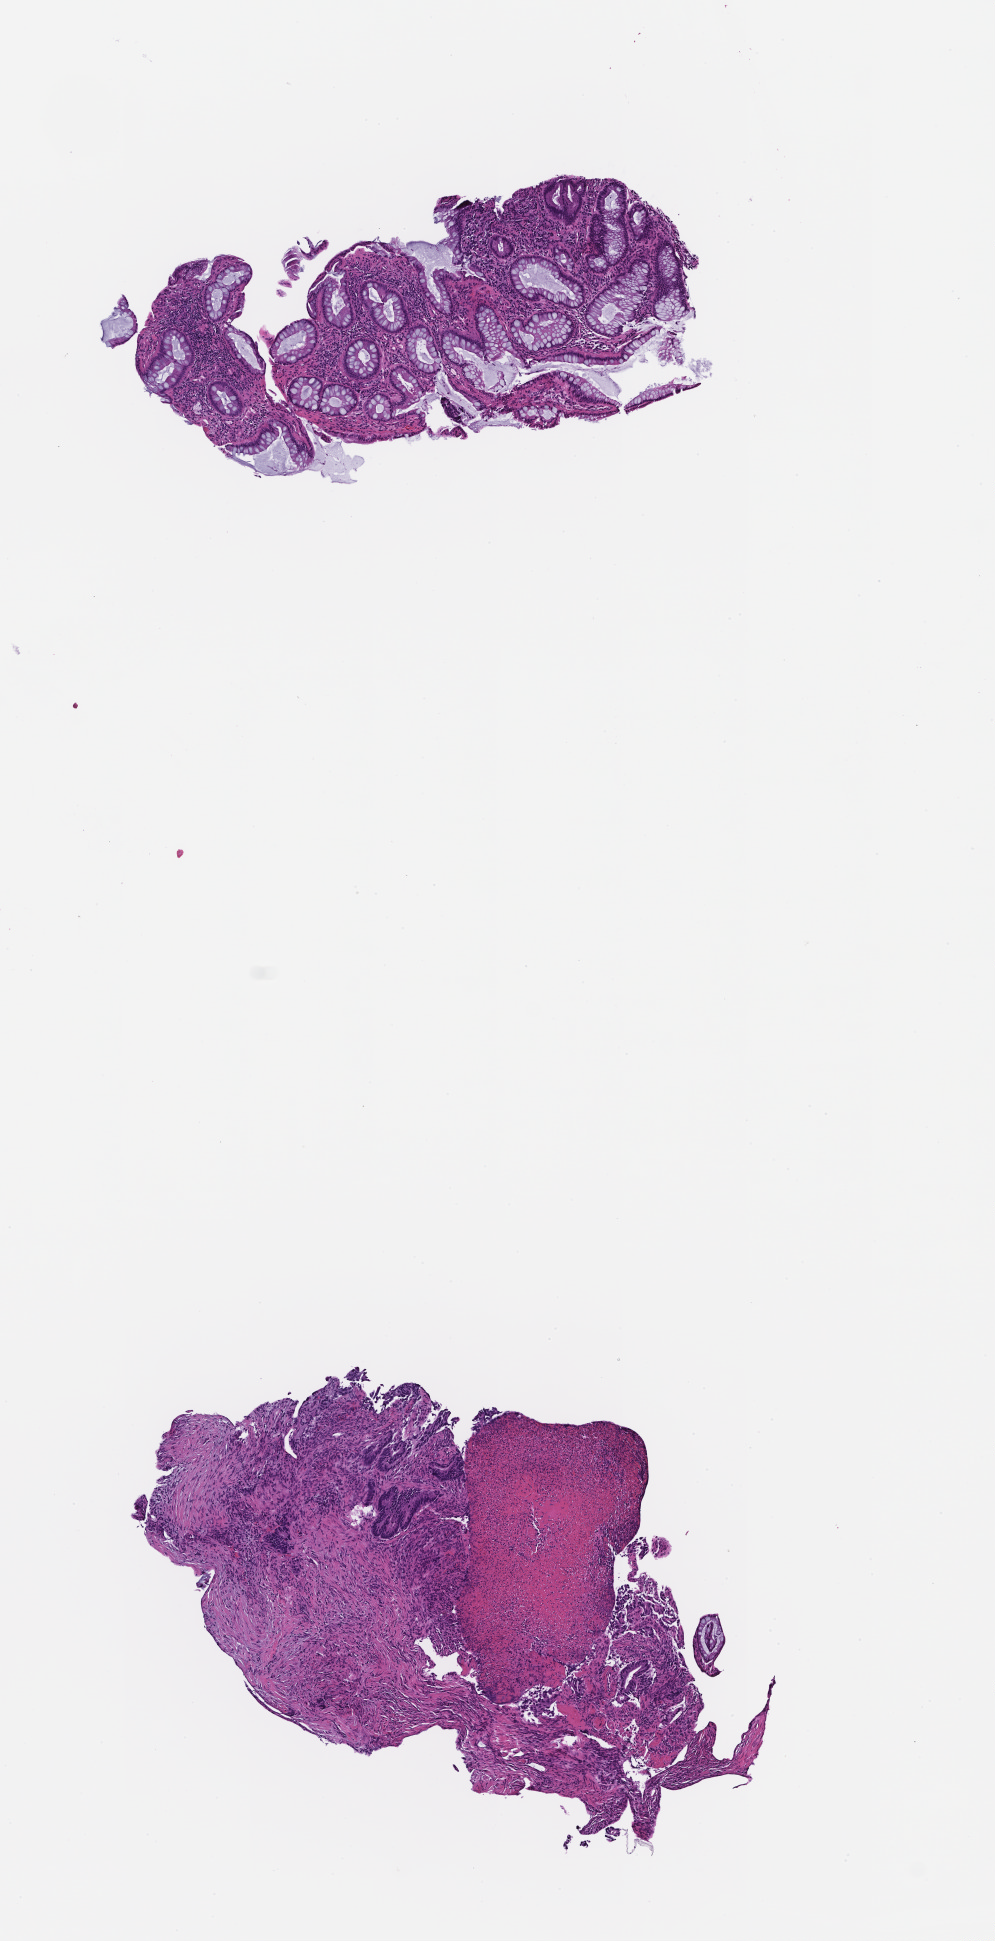
Whole-slide image, H&E stain — shown as a low-resolution overview of the whole scanned area (about 4.0 x 7.8 mm). Formalin-fixed paraffin-embedded section. Tissue site: colon. Specimen time point: collected at baseline (before treatment). Female patient.
This section: primary tumour tissue. Diagnosis: Colorectal Carcinoma.